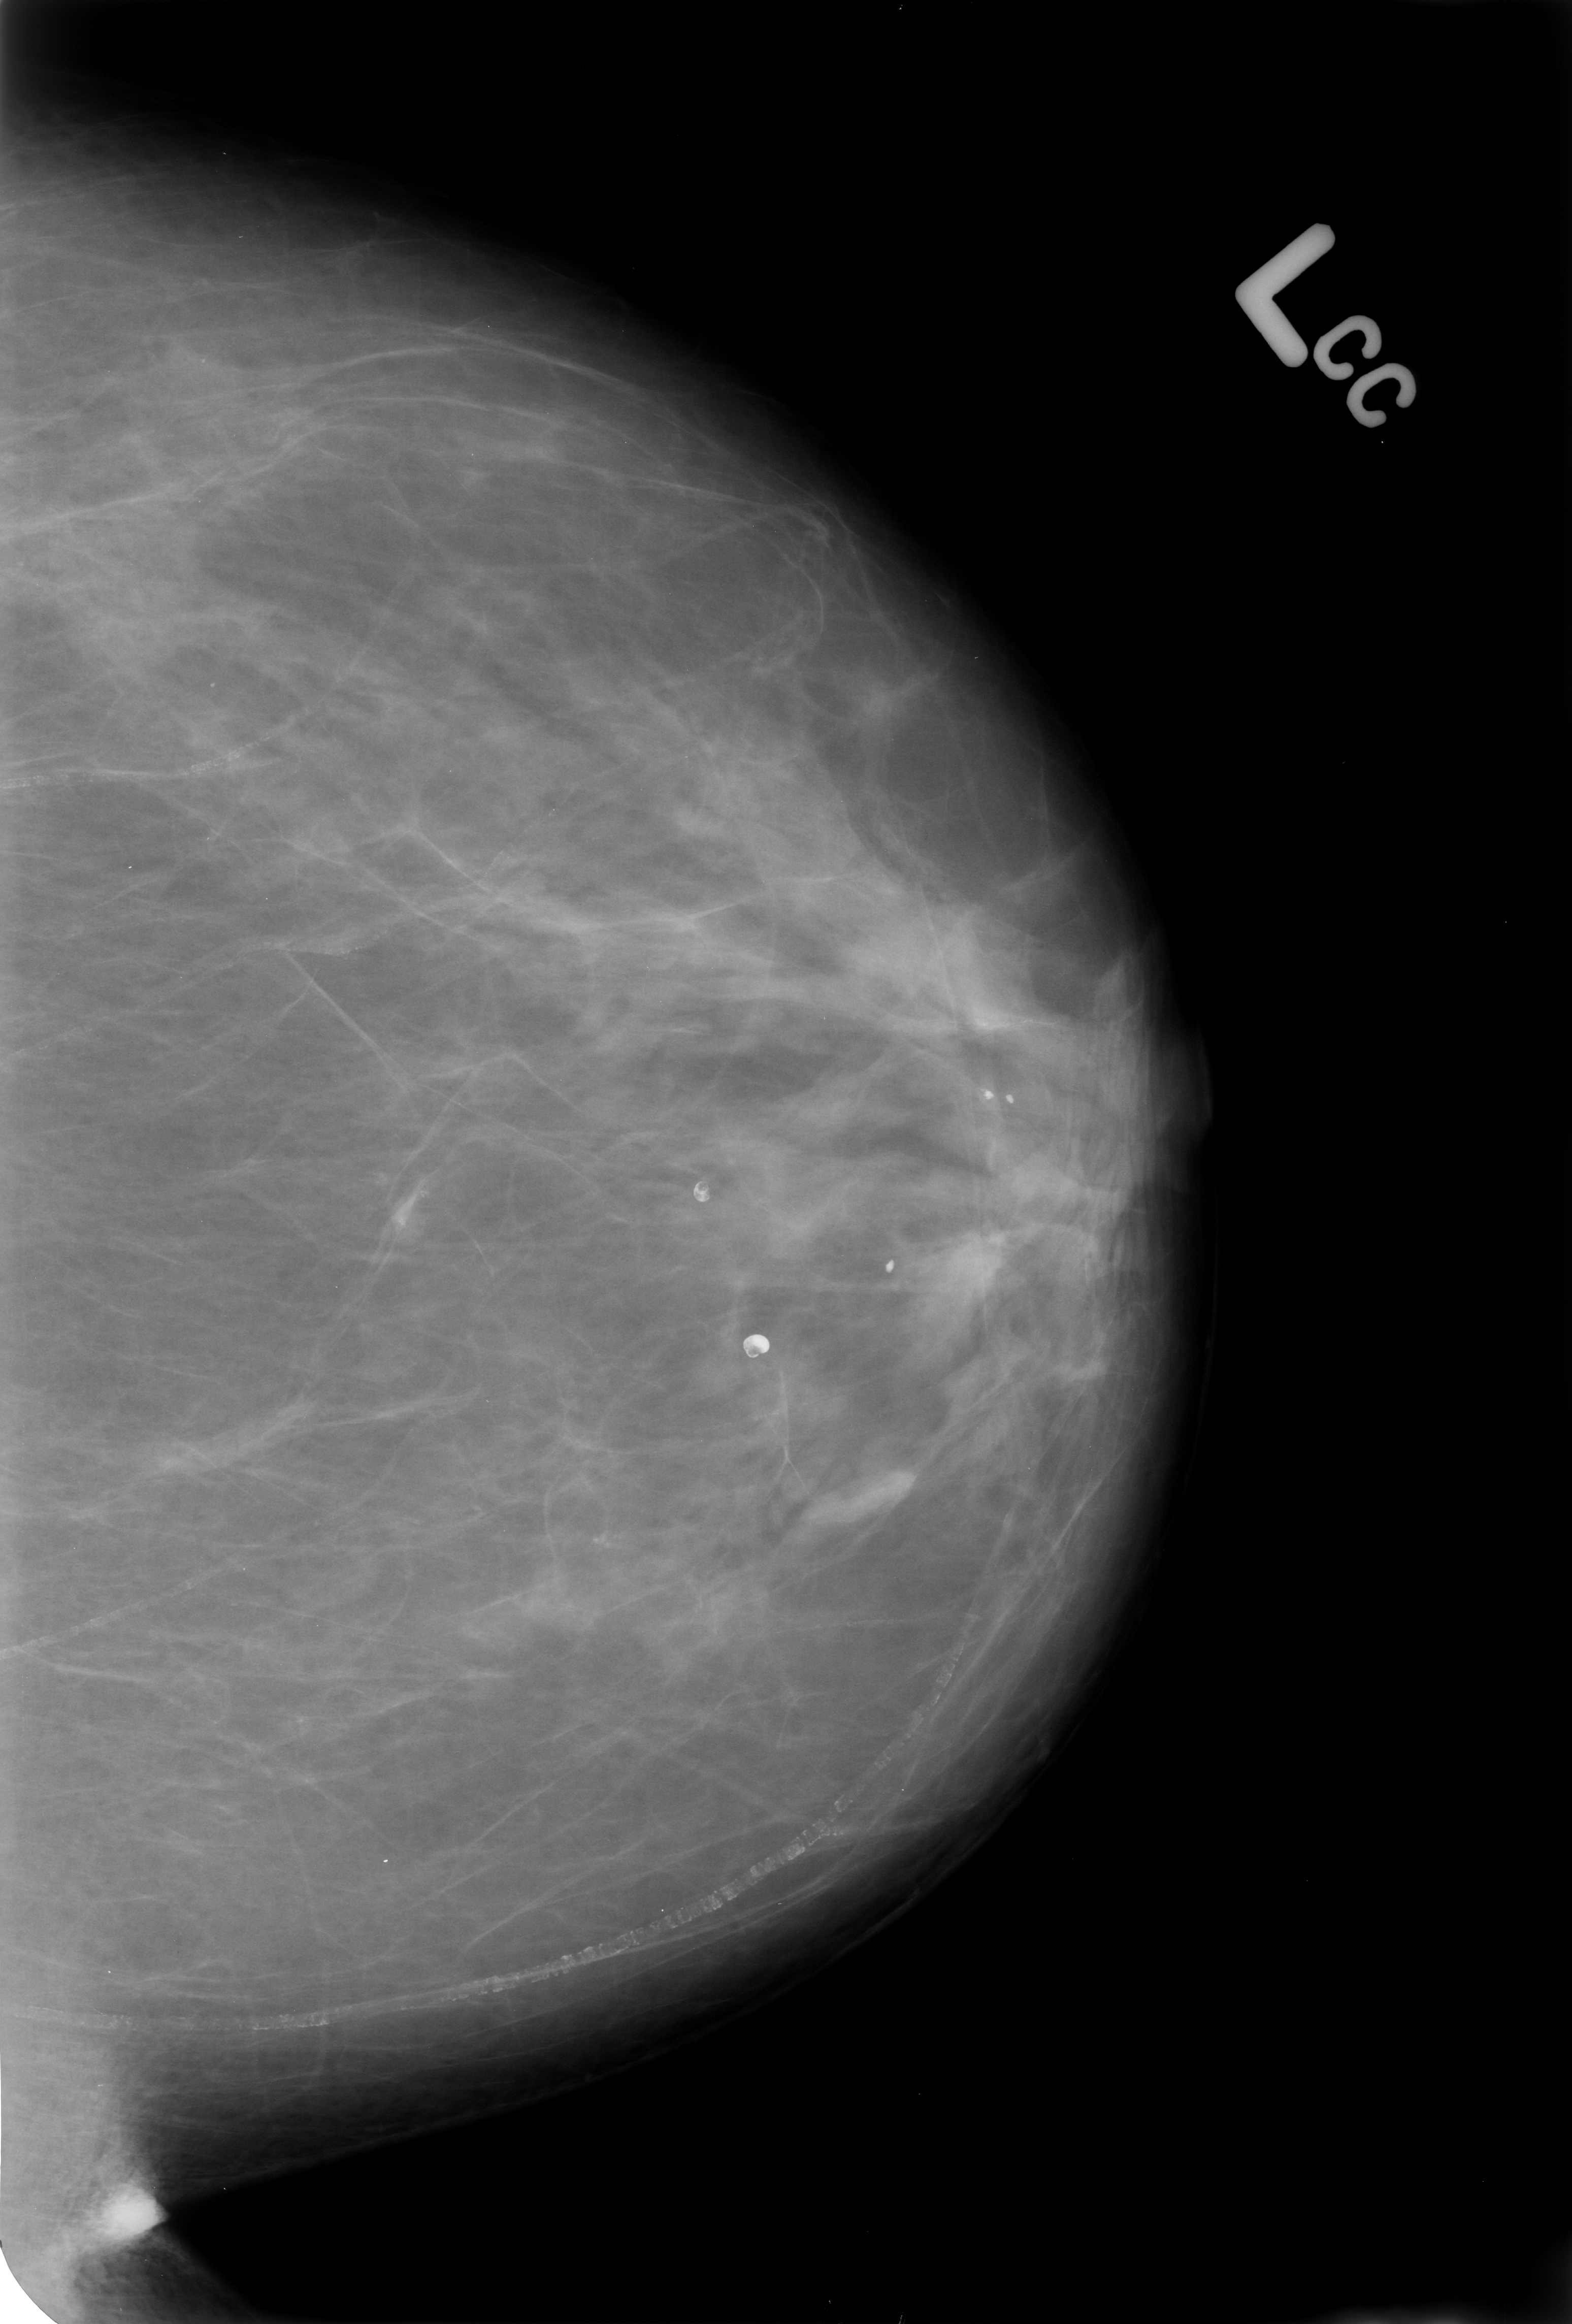
Mammogram (digitized film). Left breast. CC view. BI-RADS breast density category 2 (scale 1–4). 1572 × 2324 image matrix.
Marked abnormalities (boxes around the expert regions of interest):
- Finding 1 of 4: calcifications, morphology vascular / coarse / lucent centered; BI-RADS assessment category 2; benign; no additional work-up was recommended (outcome (as recorded, no biopsy): benign without callback): box from (x=0, y=544) to (x=452, y=814) px
- Finding 2 of 4: calcifications, morphology vascular / coarse / lucent centered; BI-RADS assessment category 2; subtlety rating 5 on a 1 (subtle) to 5 (obvious) scale; benign; no additional work-up was recommended (outcome (as recorded, no biopsy): benign without callback): (x=4, y=1718)–(x=931, y=2069)
- Finding 3 of 4: calcifications, morphology vascular / coarse / lucent centered; BI-RADS assessment category 2; benign; no additional work-up was recommended (outcome (as recorded, no biopsy): benign without callback): (x=666, y=1157)–(x=728, y=1244)
- Finding 4 of 4: calcifications, morphology vascular / coarse / lucent centered; BI-RADS assessment category 2; subtlety rating 5 on a 1 (subtle) to 5 (obvious) scale; benign; no additional work-up was recommended (outcome (as recorded, no biopsy): benign without callback): (x=723, y=1304)–(x=789, y=1395)